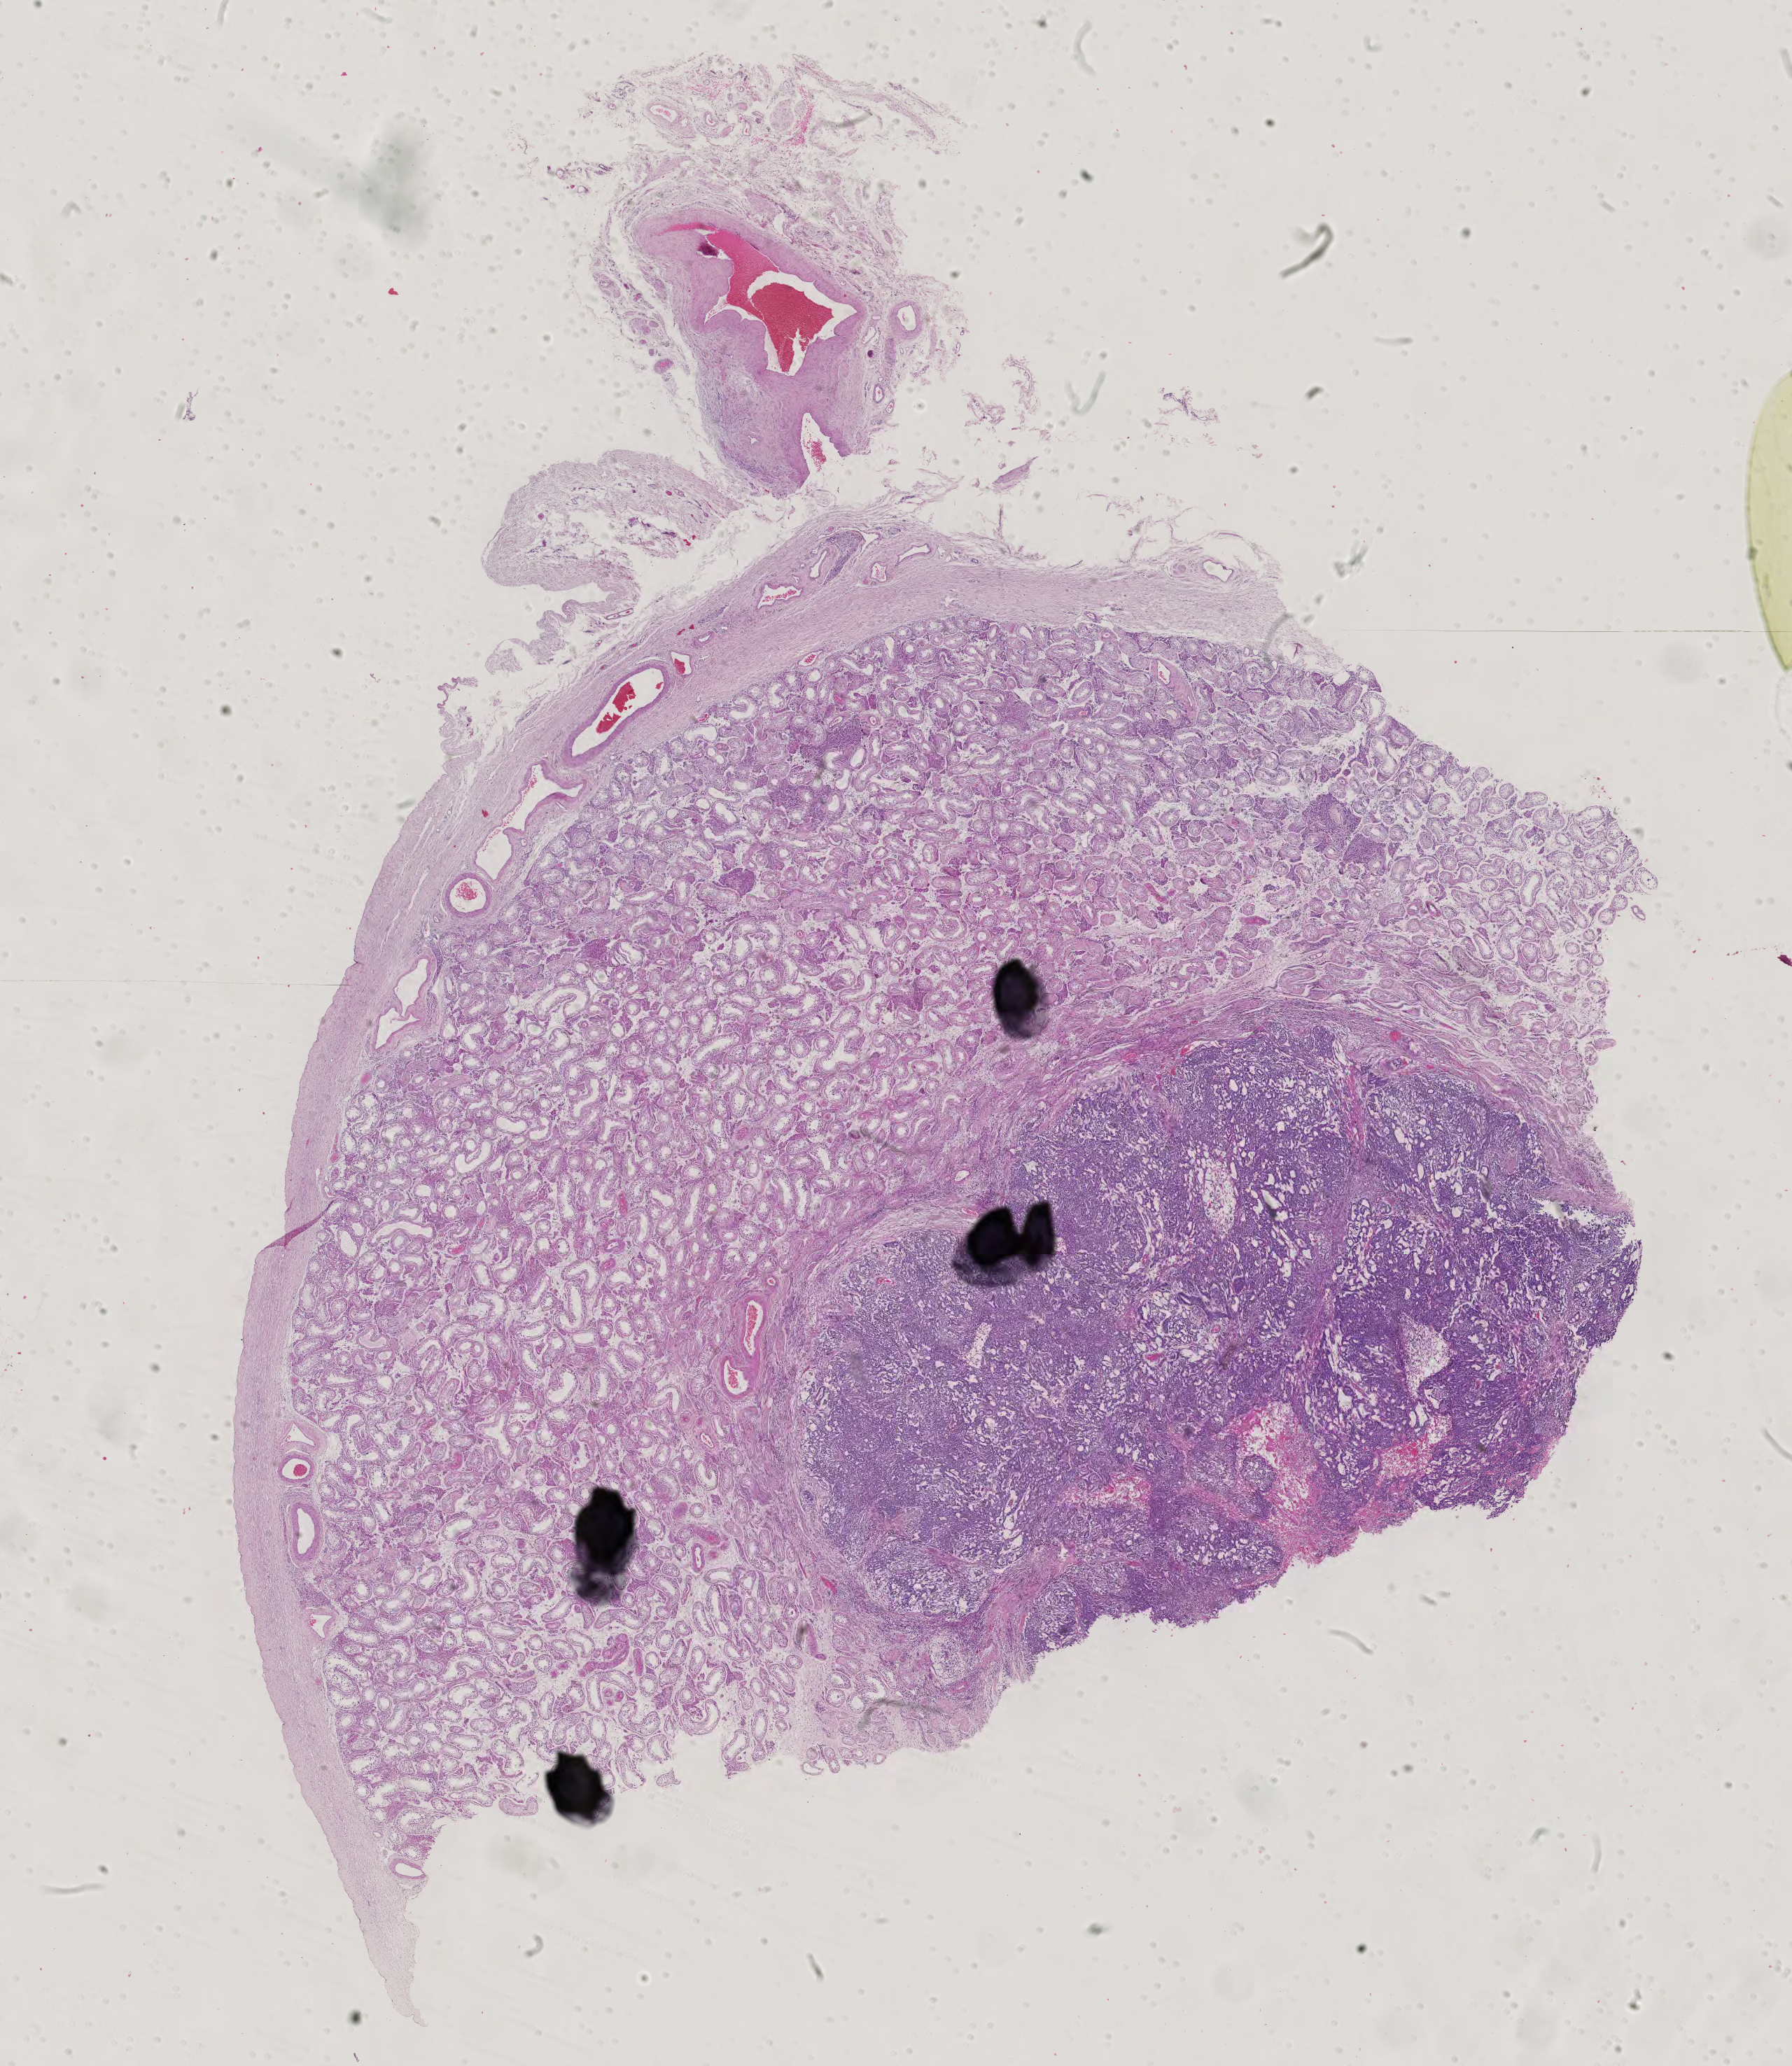
H&E-stained whole-slide image — a low-resolution overview of the entire scanned area, about 18.7 x 21.5 mm (slide scanned at 40x), formalin-fixed paraffin-embedded (FFPE) diagnostic section, sample: primary tumour, testis. Patient: male, age at initial diagnosis 31 years.
* histologic diagnosis: Yolk sac tumor
* AJCC pathologic stage: IS (7th edition)
* laterality: left
* TNM: T1 N0 M0